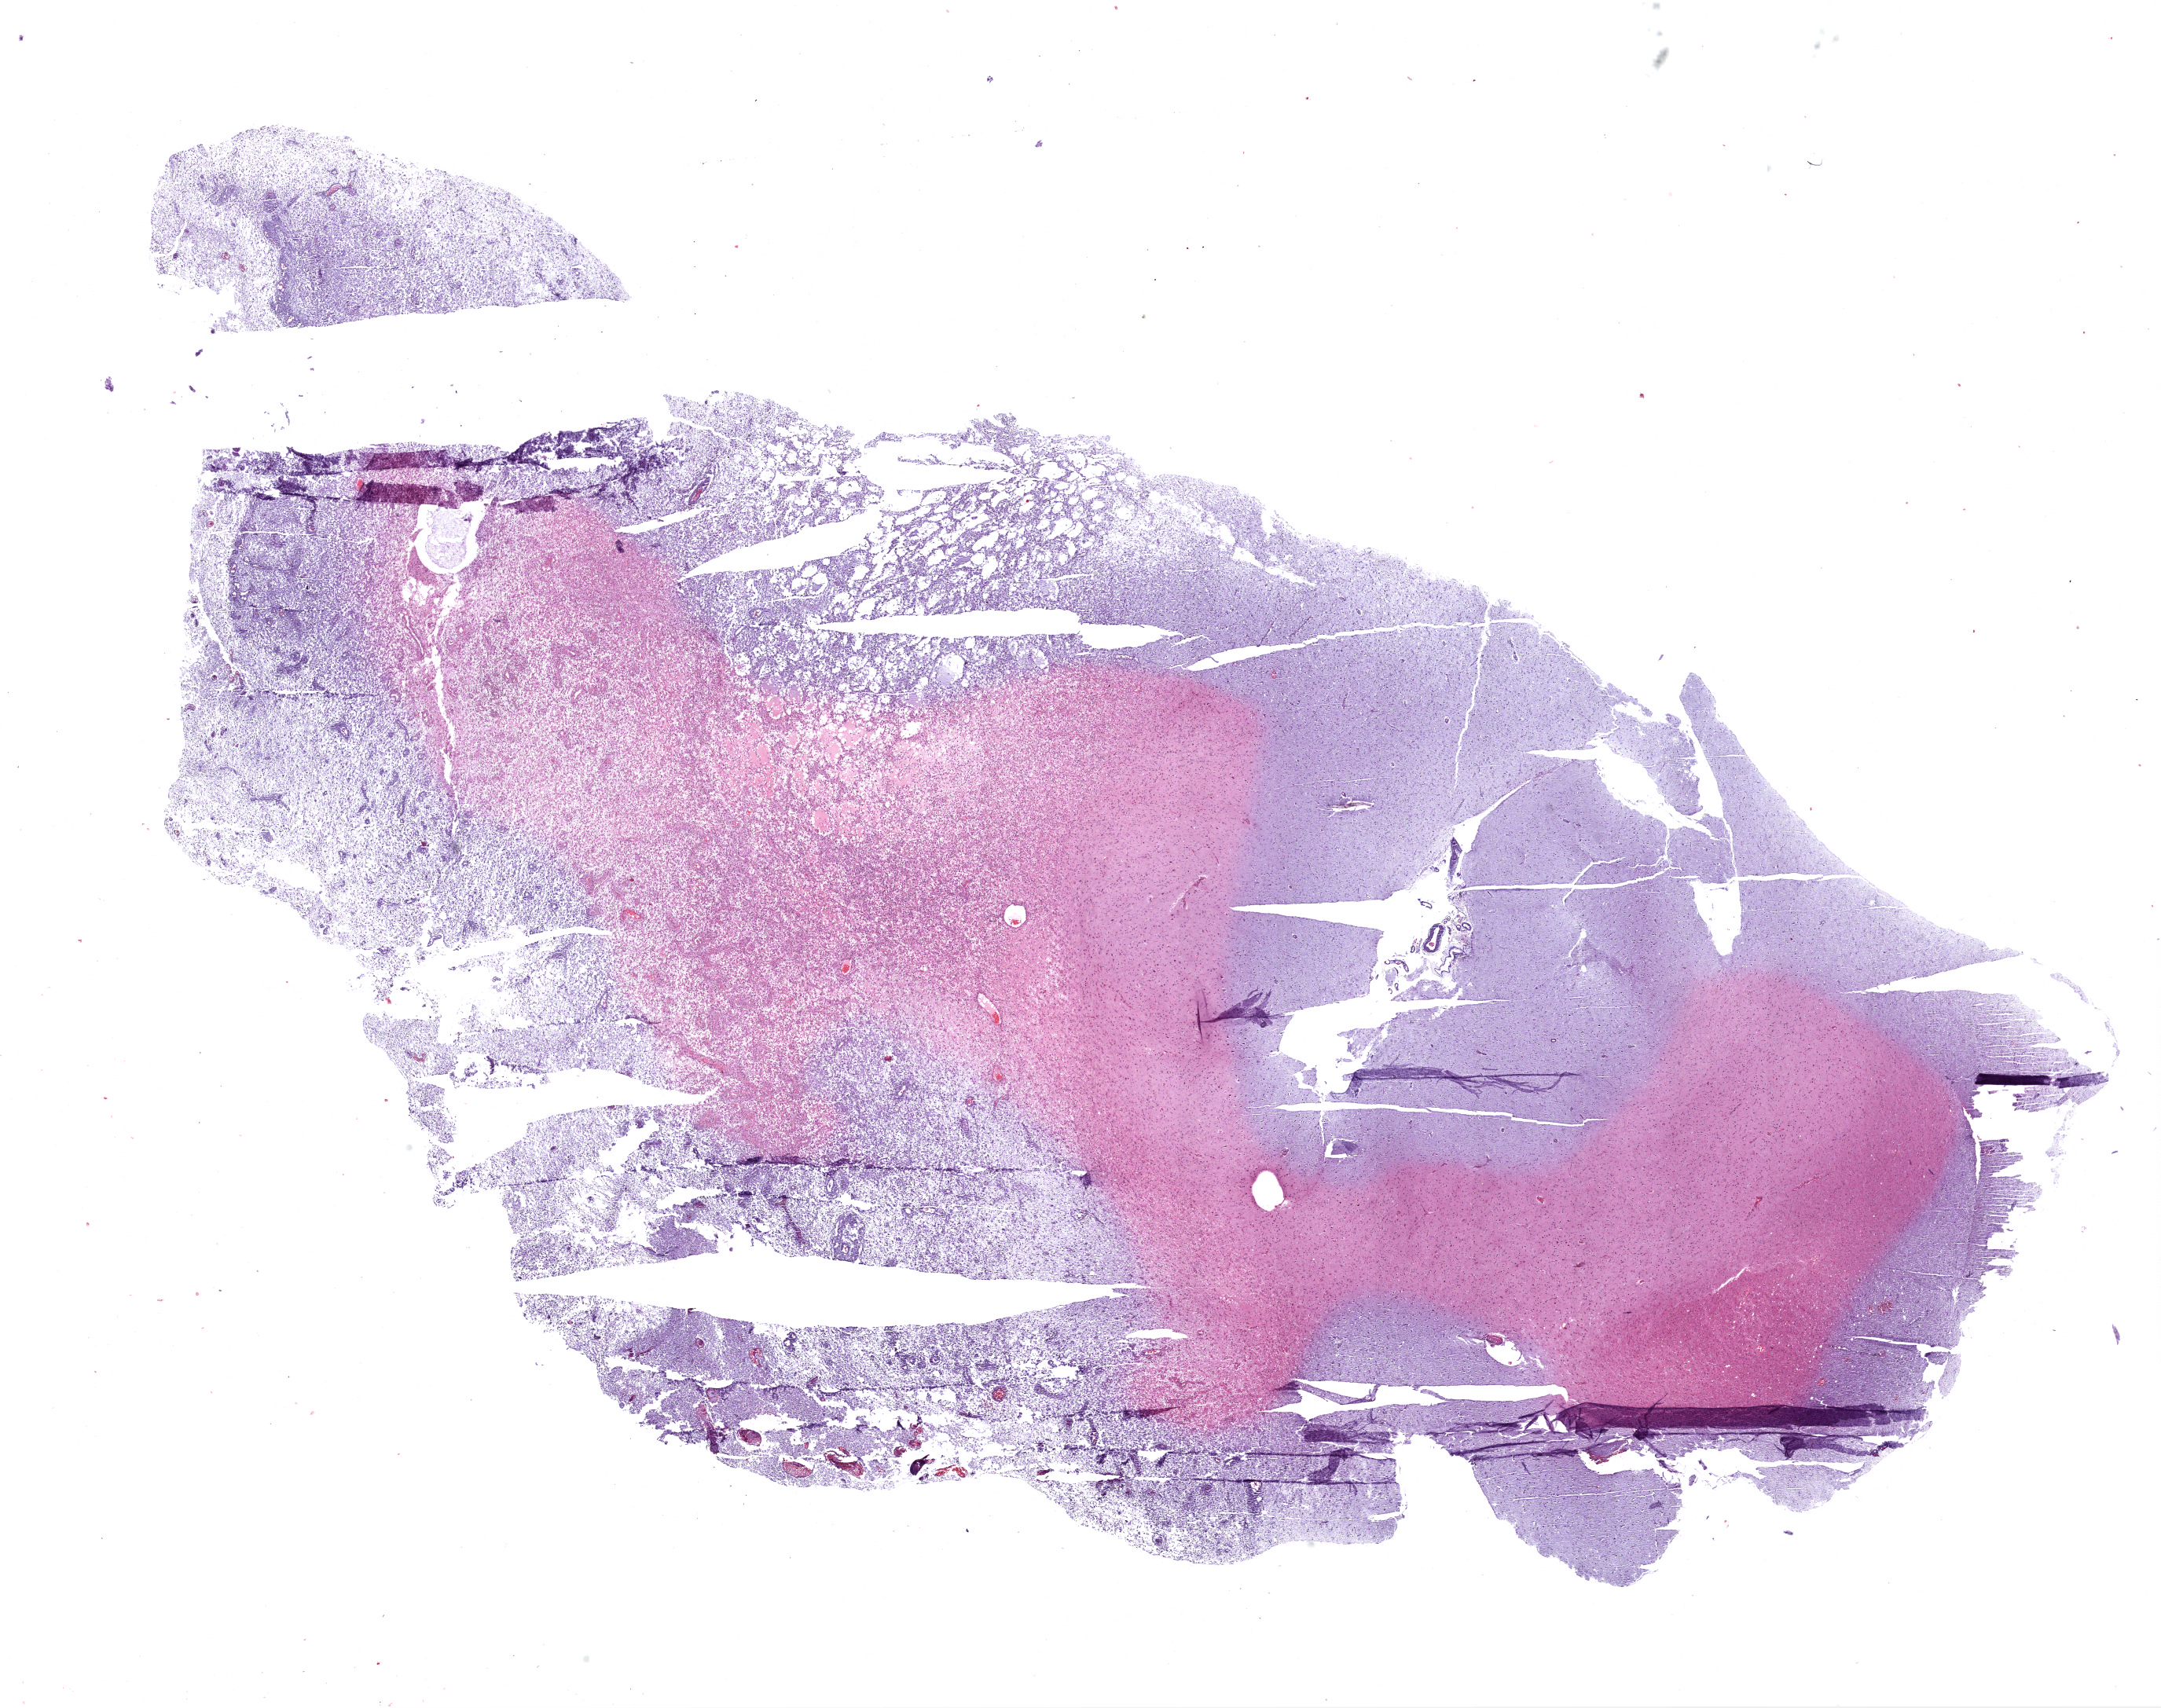
Hematoxylin and eosin (H&E) stained whole-slide image — a low-resolution overview of the entire scanned area, about 22.1 x 17.4 mm (acquisition: 20x scan), FFPE section, primary tumour sample from the brain. Male patient; age at initial diagnosis 61 years.
Histologic diagnosis: Glioblastoma.